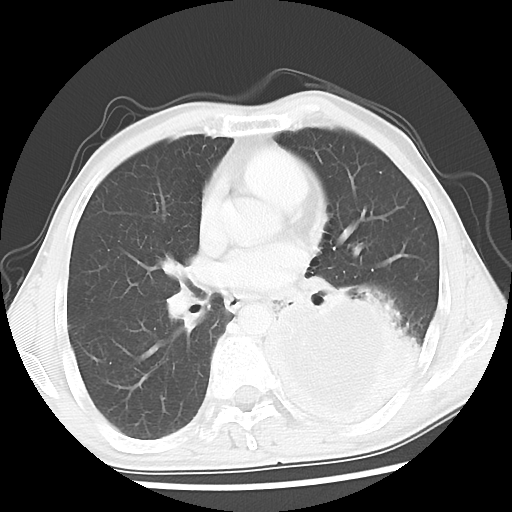
Chest CT, one axial slice. Position 25 of 52 along the scan axis. Lung window (W 1500 / L -600 HU). 5 mm slice thickness. 512 × 512 image matrix, field of view 318 × 318 mm. Male patient, age 60 years. Case-level facts recorded for this patient, not image findings: clinical TNM (as recorded): T4 N0 M0.
Outlined on this slice (bounding box drawn by a radiologist):
- lung tumour (recorded histology: squamous cell carcinoma): box from (x=260, y=286) to (x=435, y=446) px